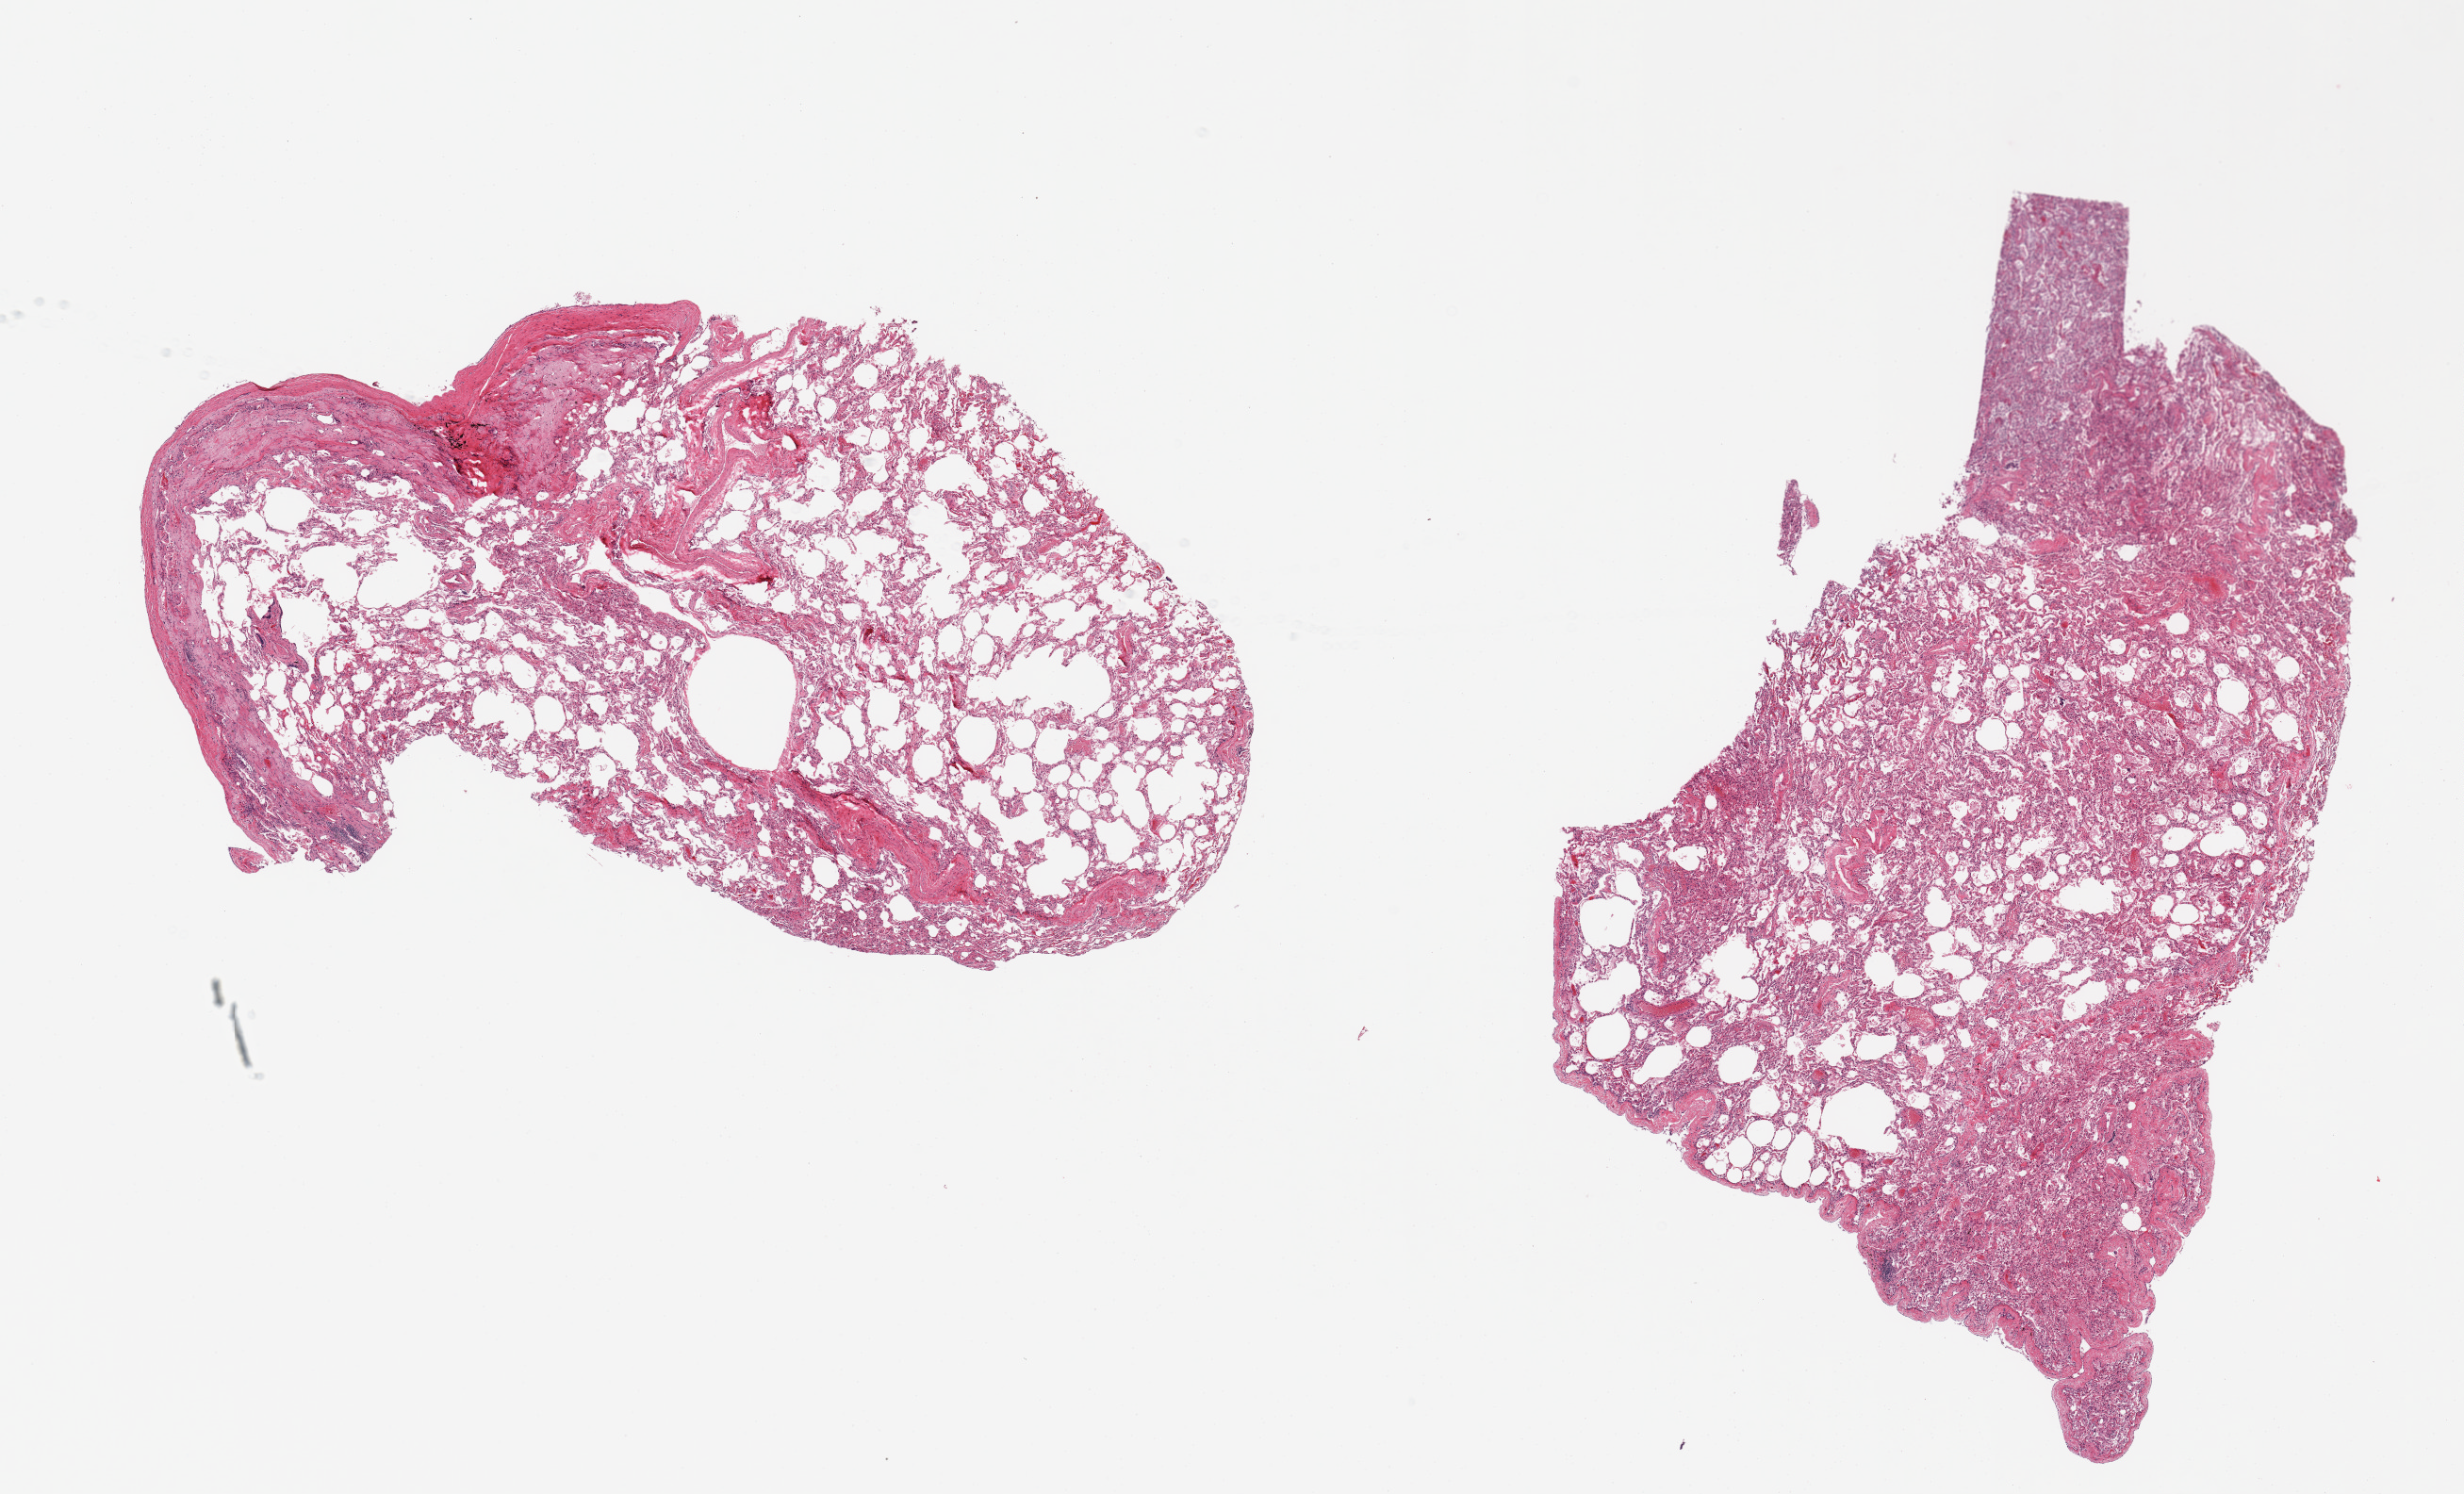
Whole-slide image, haematoxylin and eosin stain, brightfield, shown as a low-resolution overview of the whole scanned area (about 20.7 x 12.5 mm); PAXgene-fixed, paraffin-embedded tissue; section of lung (target tissue); donor tissue sample. Donor: male.
• pathologist's review note for this sample: 2 pieces; thick pleura covering 1/3 of the surface of 1 piece; segmental atelectasis emphysema